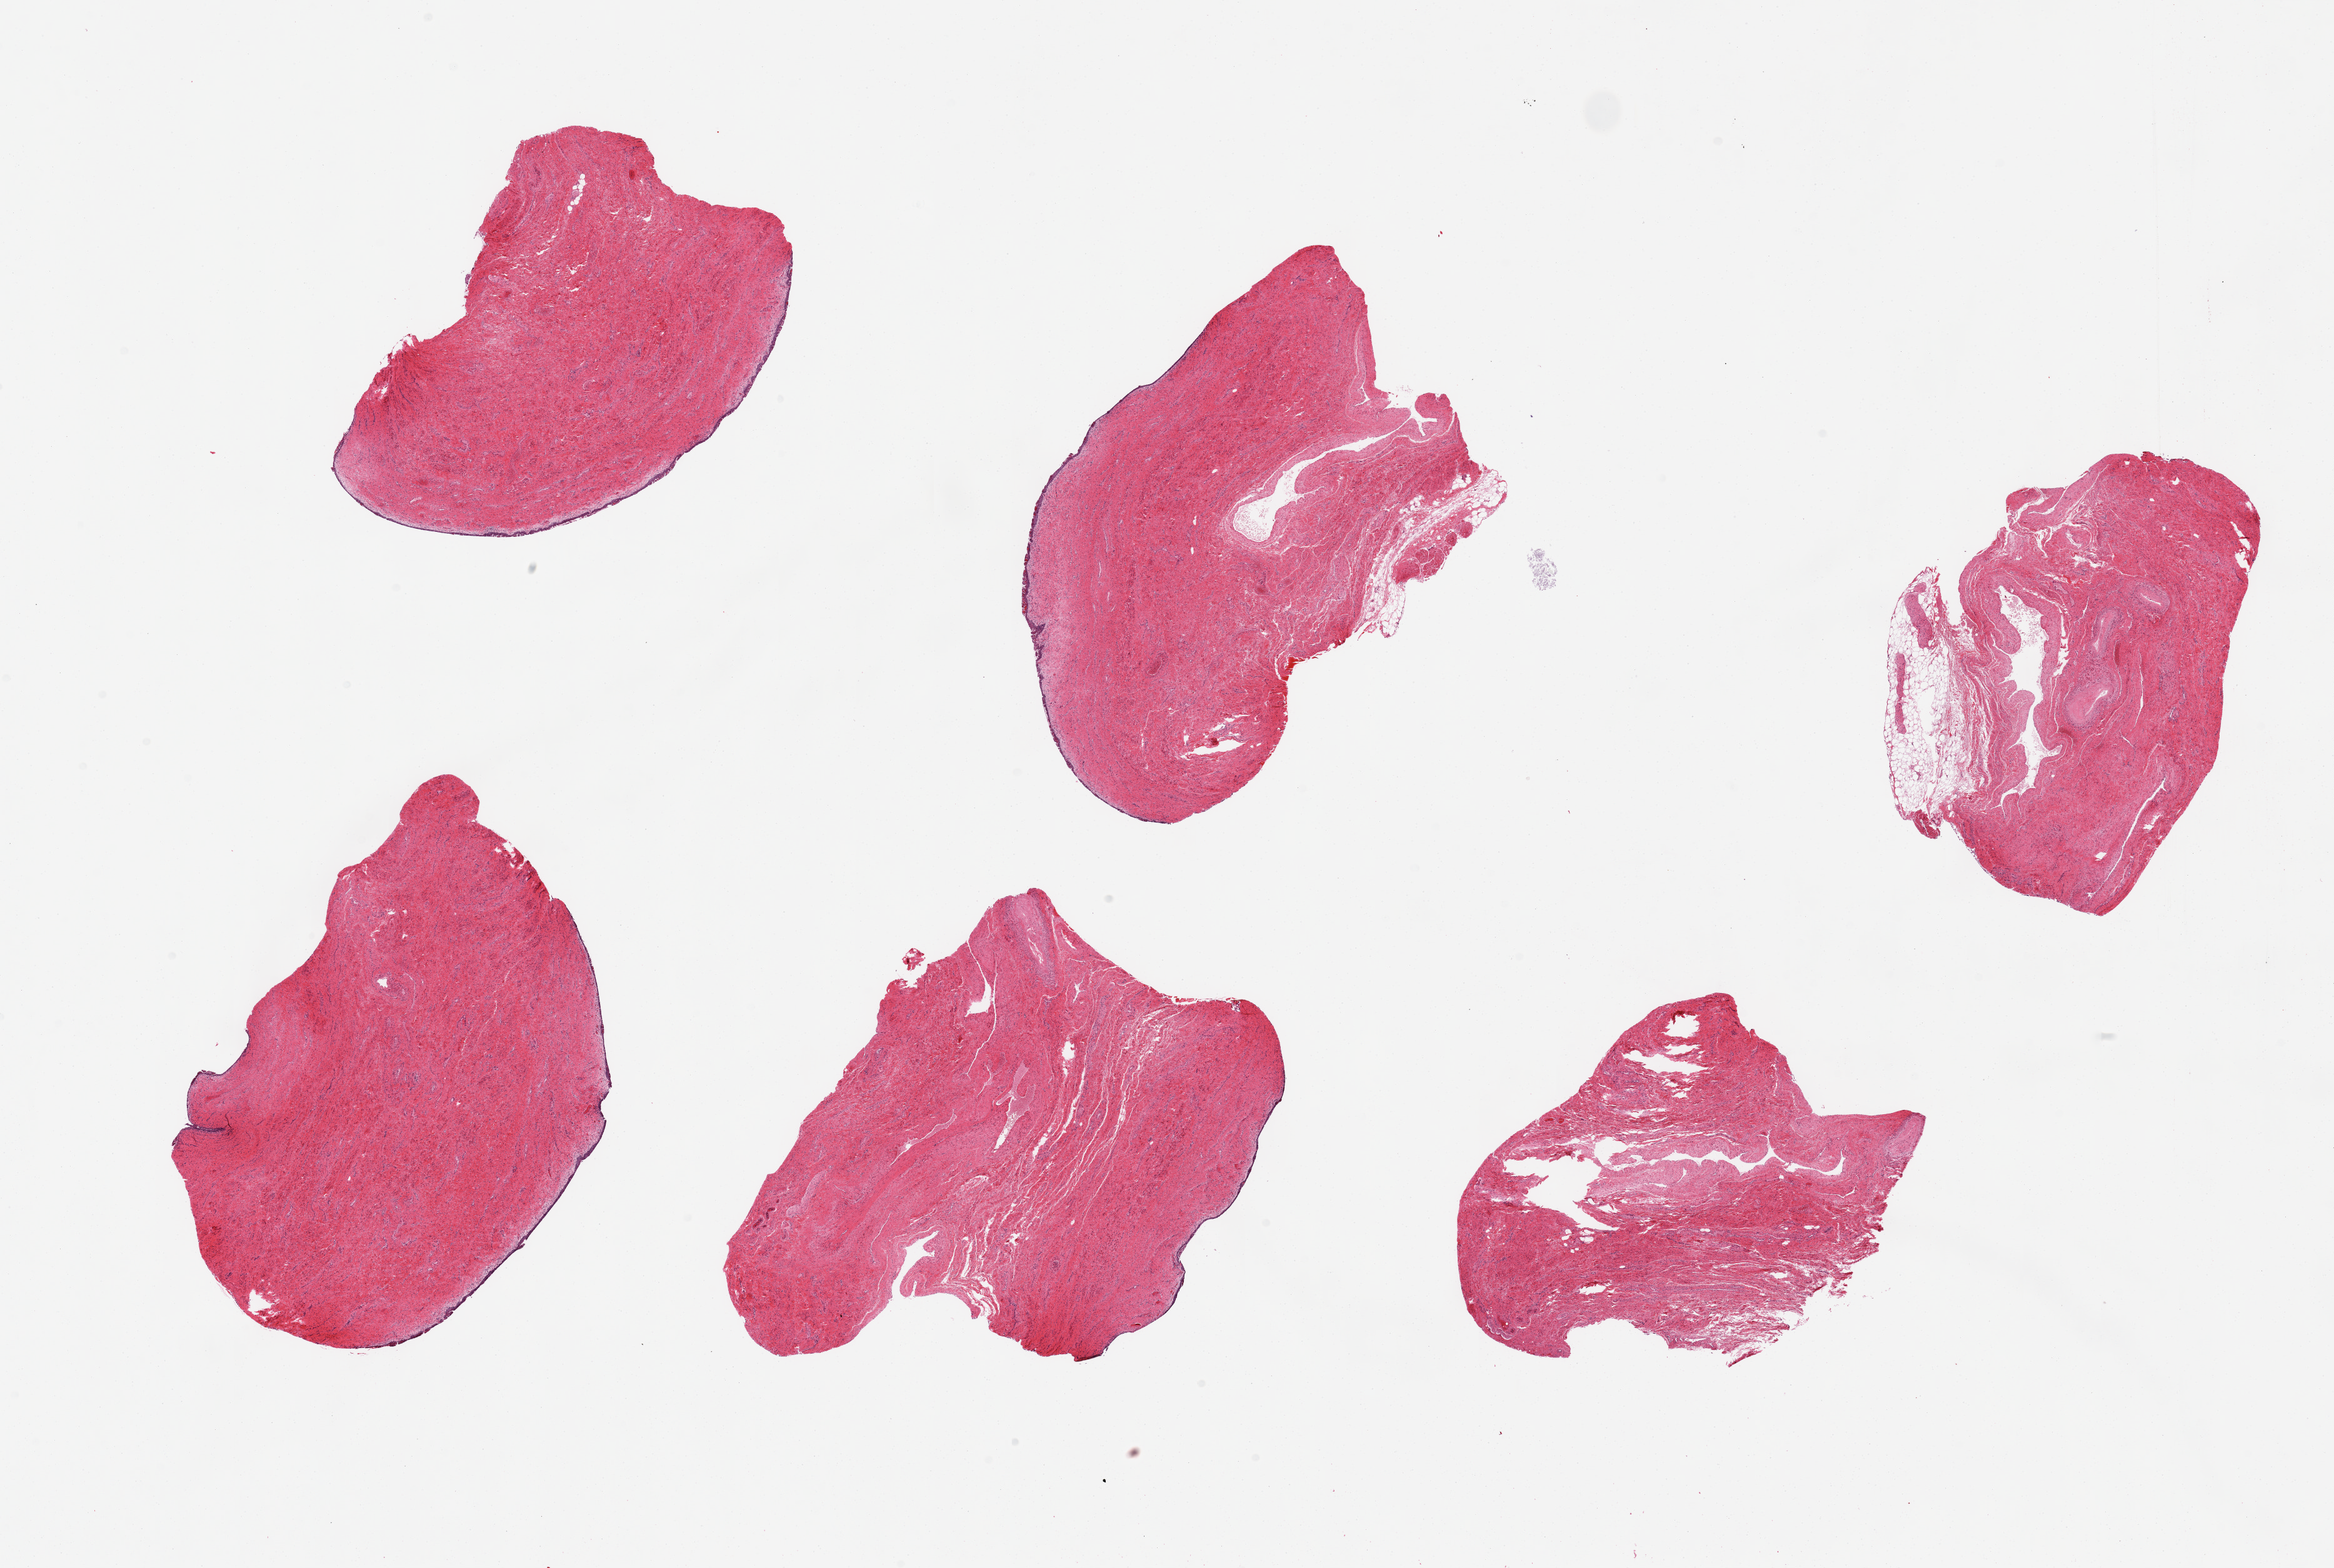
Hematoxylin and eosin (H&E) whole-slide image — whole scanned area (about 29.5 x 19.8 mm) shown as a low-resolution overview; PAXgene-fixed paraffin-embedded (PFPE) section; target tissue: vagina; donor tissue sample.
Pathologist's review note for this sample: 6 pieces, epithelium is partially denuded, 2 of 6 pieces do not show epithelium.